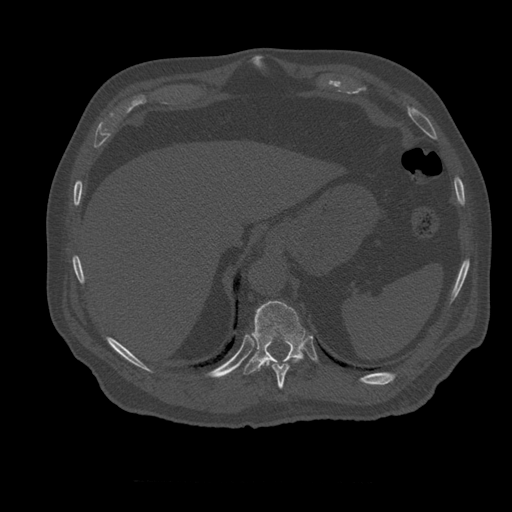
CT including the spine, one axial slice; position 288 of 399 along the scan axis; reconstruction kernel STANDARD; 120 kVp; bone window (W 1800 / L 400 HU); 1.25 mm slice thickness; 512 × 512 image matrix, field of view 407 × 407 mm. Patient age 73 years. Case-level facts recorded for this patient, not image findings: primary cancer: prostate; vertebrae with lytic lesions (as recorded): L2.
Structures marked on this image (semi-automatically segmented with operator editing):
- T10 vertebra: bounding box (x1, y1, x2, y2) in pixels: (264, 361, 302, 389)
- T11 vertebra: (244, 301, 306, 375)